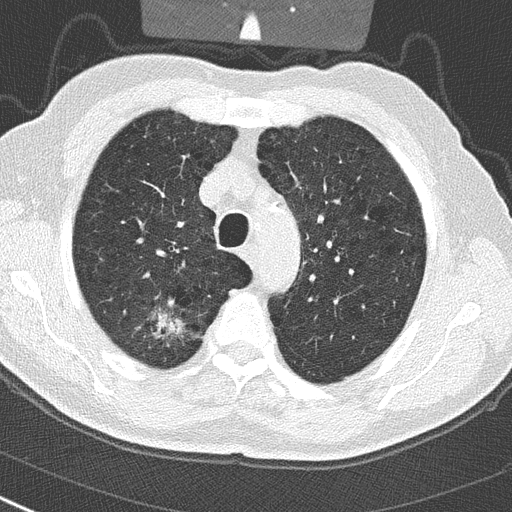
Low-dose screening chest CT, one axial slice. Position 222 of 290 along the scan axis. 120 kVp. Lung window (W 1500 / L -600 HU). 2 mm slice thickness. 512 × 512 image matrix.
Annotated regions visible in this slice (manually delineated by an expert):
- lesion 1 (tumor, upper lobe of right lung): bounding box <151,313,189,347> (left, top, right, bottom; pixels)